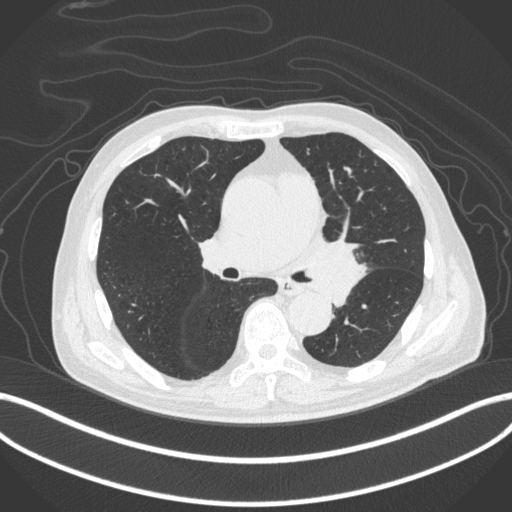
Chest CT, one axial slice. 120 kVp. Lung window (W 1500 / L -600 HU). 1 mm slice thickness. 512 × 512 image matrix, field of view 400 × 400 mm. Patient: male, 77 years. From the clinical record (not read from this slice): clinical TNM (as recorded): T3 N1 M0.
Outlined on this slice (bounding box drawn by a radiologist):
- lung tumour (recorded histology: adenocarcinoma): bounding box (x1, y1, x2, y2) in pixels: (304, 233, 365, 306)